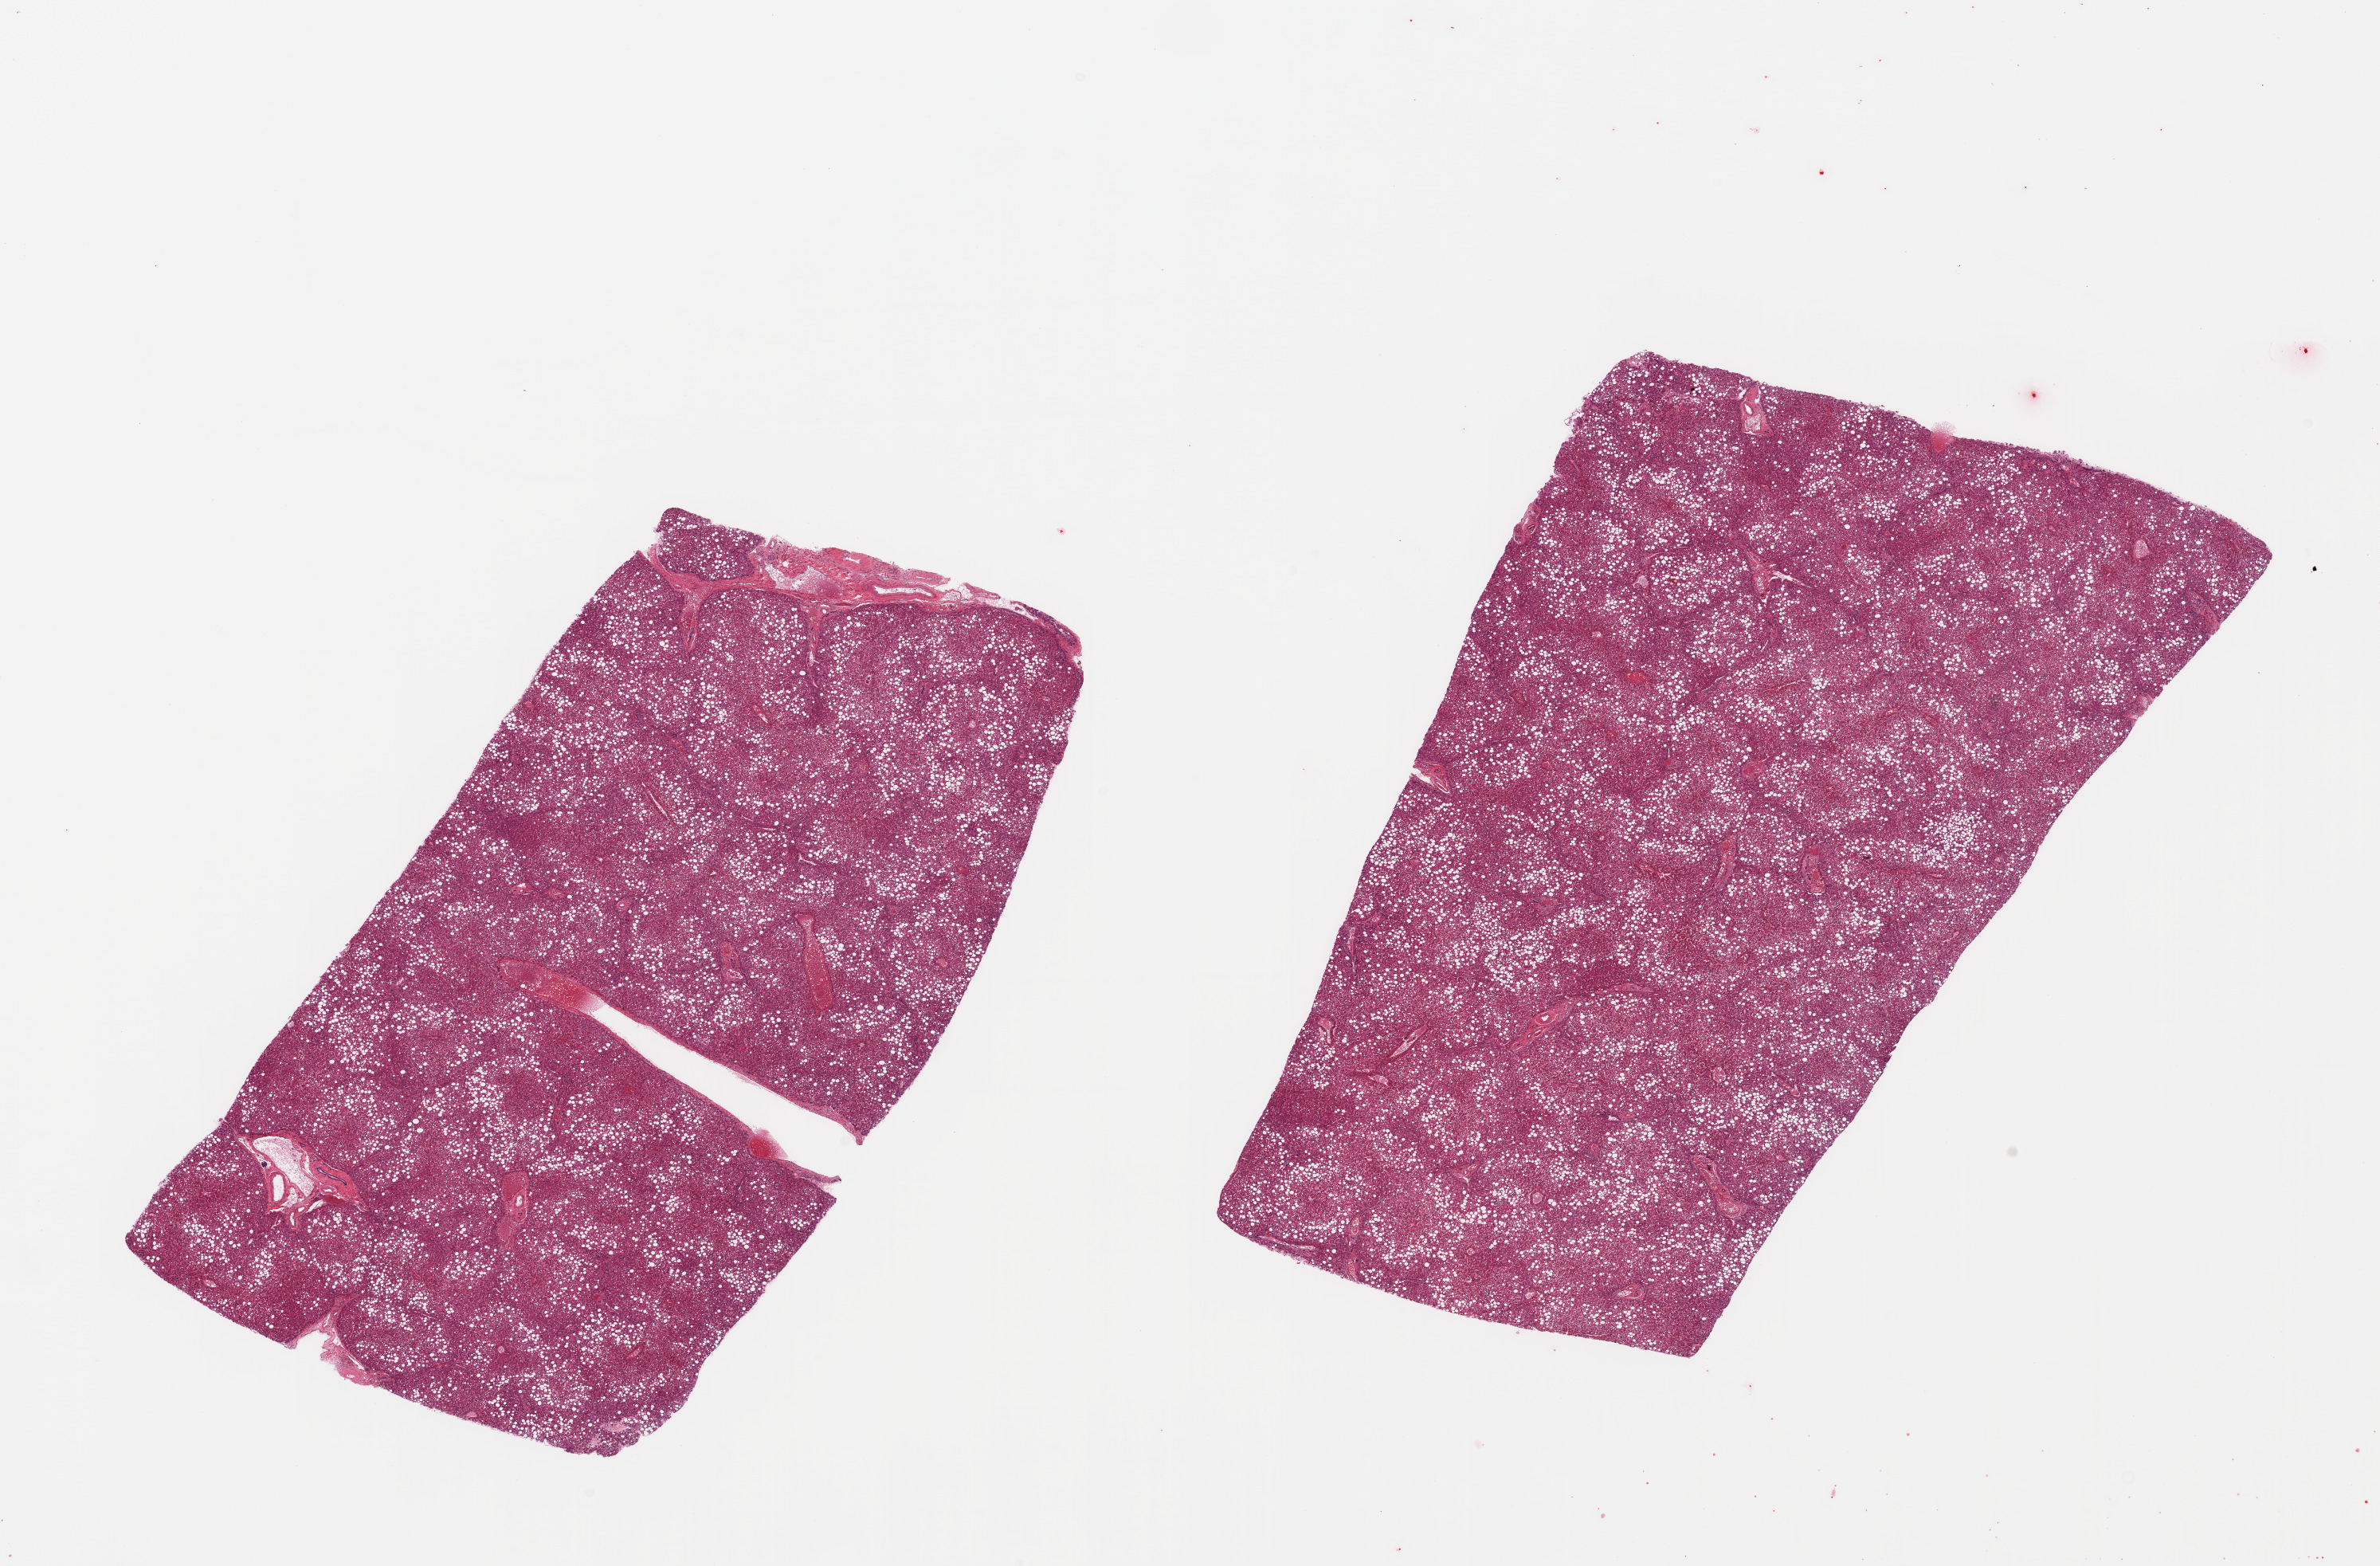
Digitized haematoxylin and eosin-stained section — whole scanned area (about 23.6 x 15.5 mm, acquisition: 20x scan) shown as a low-resolution overview, PAXgene-fixed paraffin-embedded (PFPE) section, sampled site (target tissue): liver, donor tissue sample. Female donor.
Reviewer comment on this tissue sample: 2 pieces, diffuse moderate-severe macro and microvesicular steatosis.